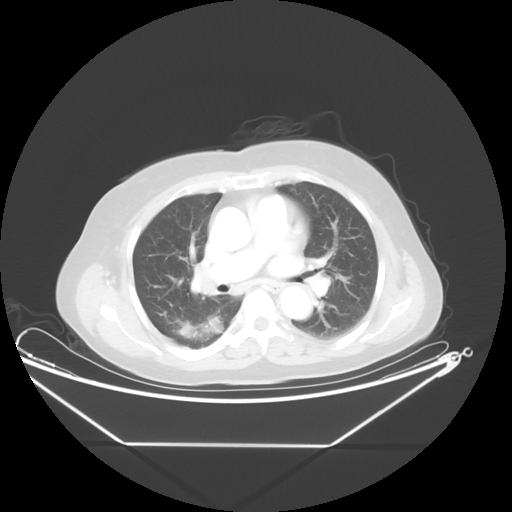
Chest CT, one axial slice. Slice 26 of 48 in the series (ordered by position). Reconstruction kernel STANDARD. 100 kVp. Lung window (W 1500 / L -600 HU). 512 × 512 image matrix, field of view 462 × 462 mm. Female patient, age 62 years. Case-level facts recorded for this patient, not image findings: clinical TNM (as recorded): T1c N0 M0; histopathological grade: G2-3.
Outlined on this slice (bounding box drawn by a radiologist):
- lung tumour (recorded histology: adenocarcinoma): bounding box [x1, y1, x2, y2] px = [166, 304, 229, 345]